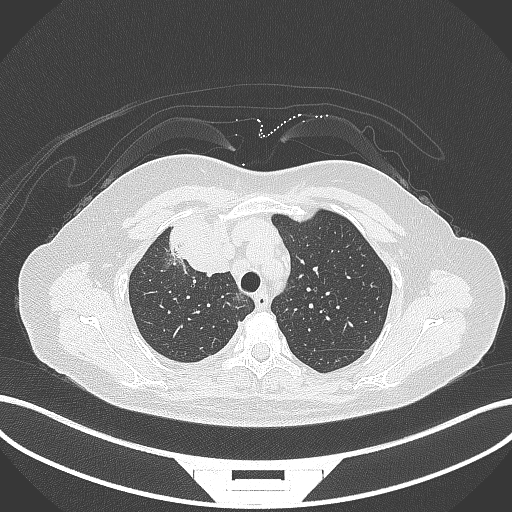
Chest CT, one axial slice; position 234 of 305 along the scan axis; 120 kVp; lung window (W 1500 / L -600 HU); 512 × 512 image matrix, field of view 400 × 400 mm. Female patient, age 52 years. Case-level facts recorded for this patient, not image findings: clinical TNM (as recorded): T3 N1 M1.
Annotated regions visible in this slice (bounding box drawn by a radiologist):
- lung tumour (recorded histology: adenocarcinoma): bounding box <165,216,236,276> (left, top, right, bottom; pixels)